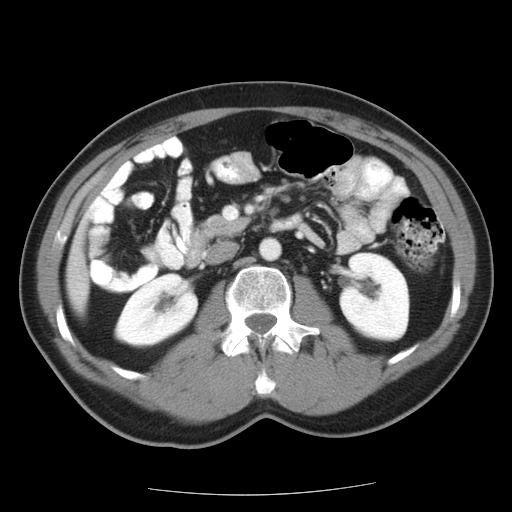
Contrast-enhanced abdominal CT, one axial slice; 120 kVp; intravenous contrast given; soft-tissue window (W 400 / L 40 HU); 7.5 mm slice thickness; 512 × 512 image matrix. Male patient, age 41 years. Case-level facts recorded for this patient, not image findings: diagnosis: colorectal cancer liver metastases, imaged before liver resection; multiple liver metastases: no; largest metastasis: 2.7 cm; disease in both lobes: no.
Structures marked on this image (outlined manually by an expert reader):
- liver: bounding box <69,244,88,301> (left, top, right, bottom; pixels)
- planned liver remnant (the part of the liver to remain after resection): <70,244,88,301>